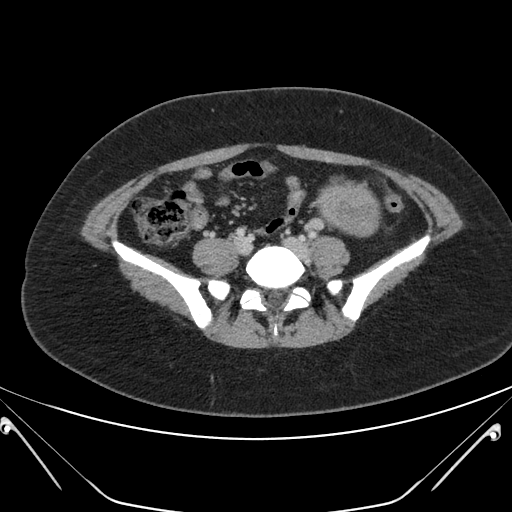
Contrast-enhanced abdominal CT, one axial slice. Position 65 of 168 along the scan axis. 120 kVp. Soft-tissue window (W 400 / L 40 HU). 512 × 512 image matrix, field of view 394 × 394 mm. Female patient, age 26 years. Case-level facts recorded for this patient, not image findings: diagnosis: adrenocortical carcinoma; tumour side: left adrenal; tumour size at pathology: 28 cm.
Annotated regions visible in this slice (semi-automatic segmentation, software-assisted and operator-edited):
- mass: bounding box [x1, y1, x2, y2] px = [322, 188, 377, 235]